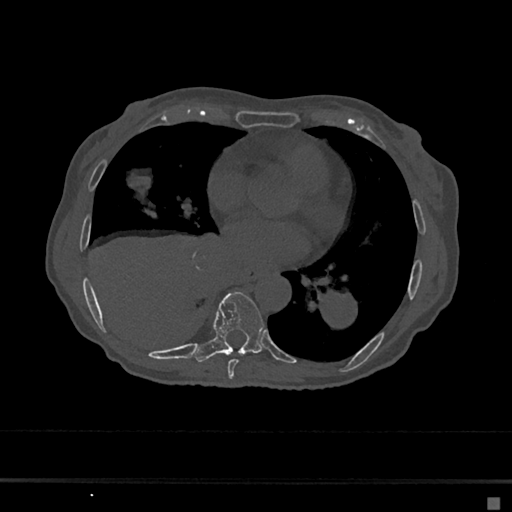
CT including the spine, one axial slice; position 337 of 797 along the scan axis; reconstruction kernel Br40s/3; 120 kVp; bone window (W 1800 / L 400 HU); 0.5 mm slice thickness; 512 × 512 image matrix. Female patient, age 68 years. From the clinical record (not read from this slice): primary cancer: renal.
Annotated regions visible in this slice (semi-automatically segmented with operator editing):
- T7 vertebra: box from (x=228, y=359) to (x=238, y=379) px
- T8 vertebra: (x=195, y=292)–(x=264, y=362)